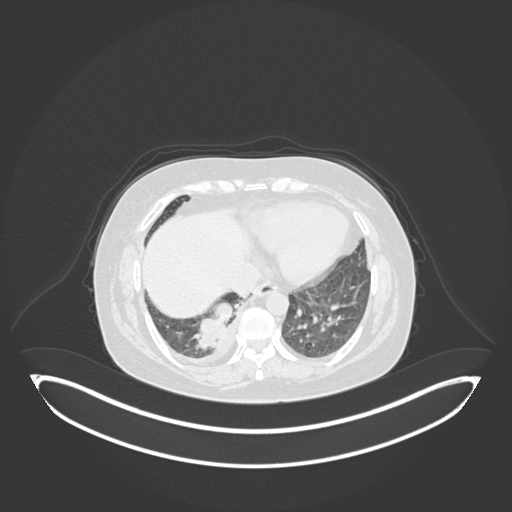
Chest CT, one axial slice; slice 38 of 231 in the series (ordered by position); lung window (W 1500 / L -600 HU); 1 mm slice thickness; 512 × 512 image matrix, field of view 500 × 500 mm. Patient: female, 56 years. From the clinical record (not read from this slice): clinical TNM (as recorded): T2b N1 M0; histopathological grade: G3.
Annotated regions visible in this slice (bounding box drawn by a radiologist):
- lung tumour (recorded histology: small cell carcinoma): bounding box [x1, y1, x2, y2] px = [189, 300, 235, 356]